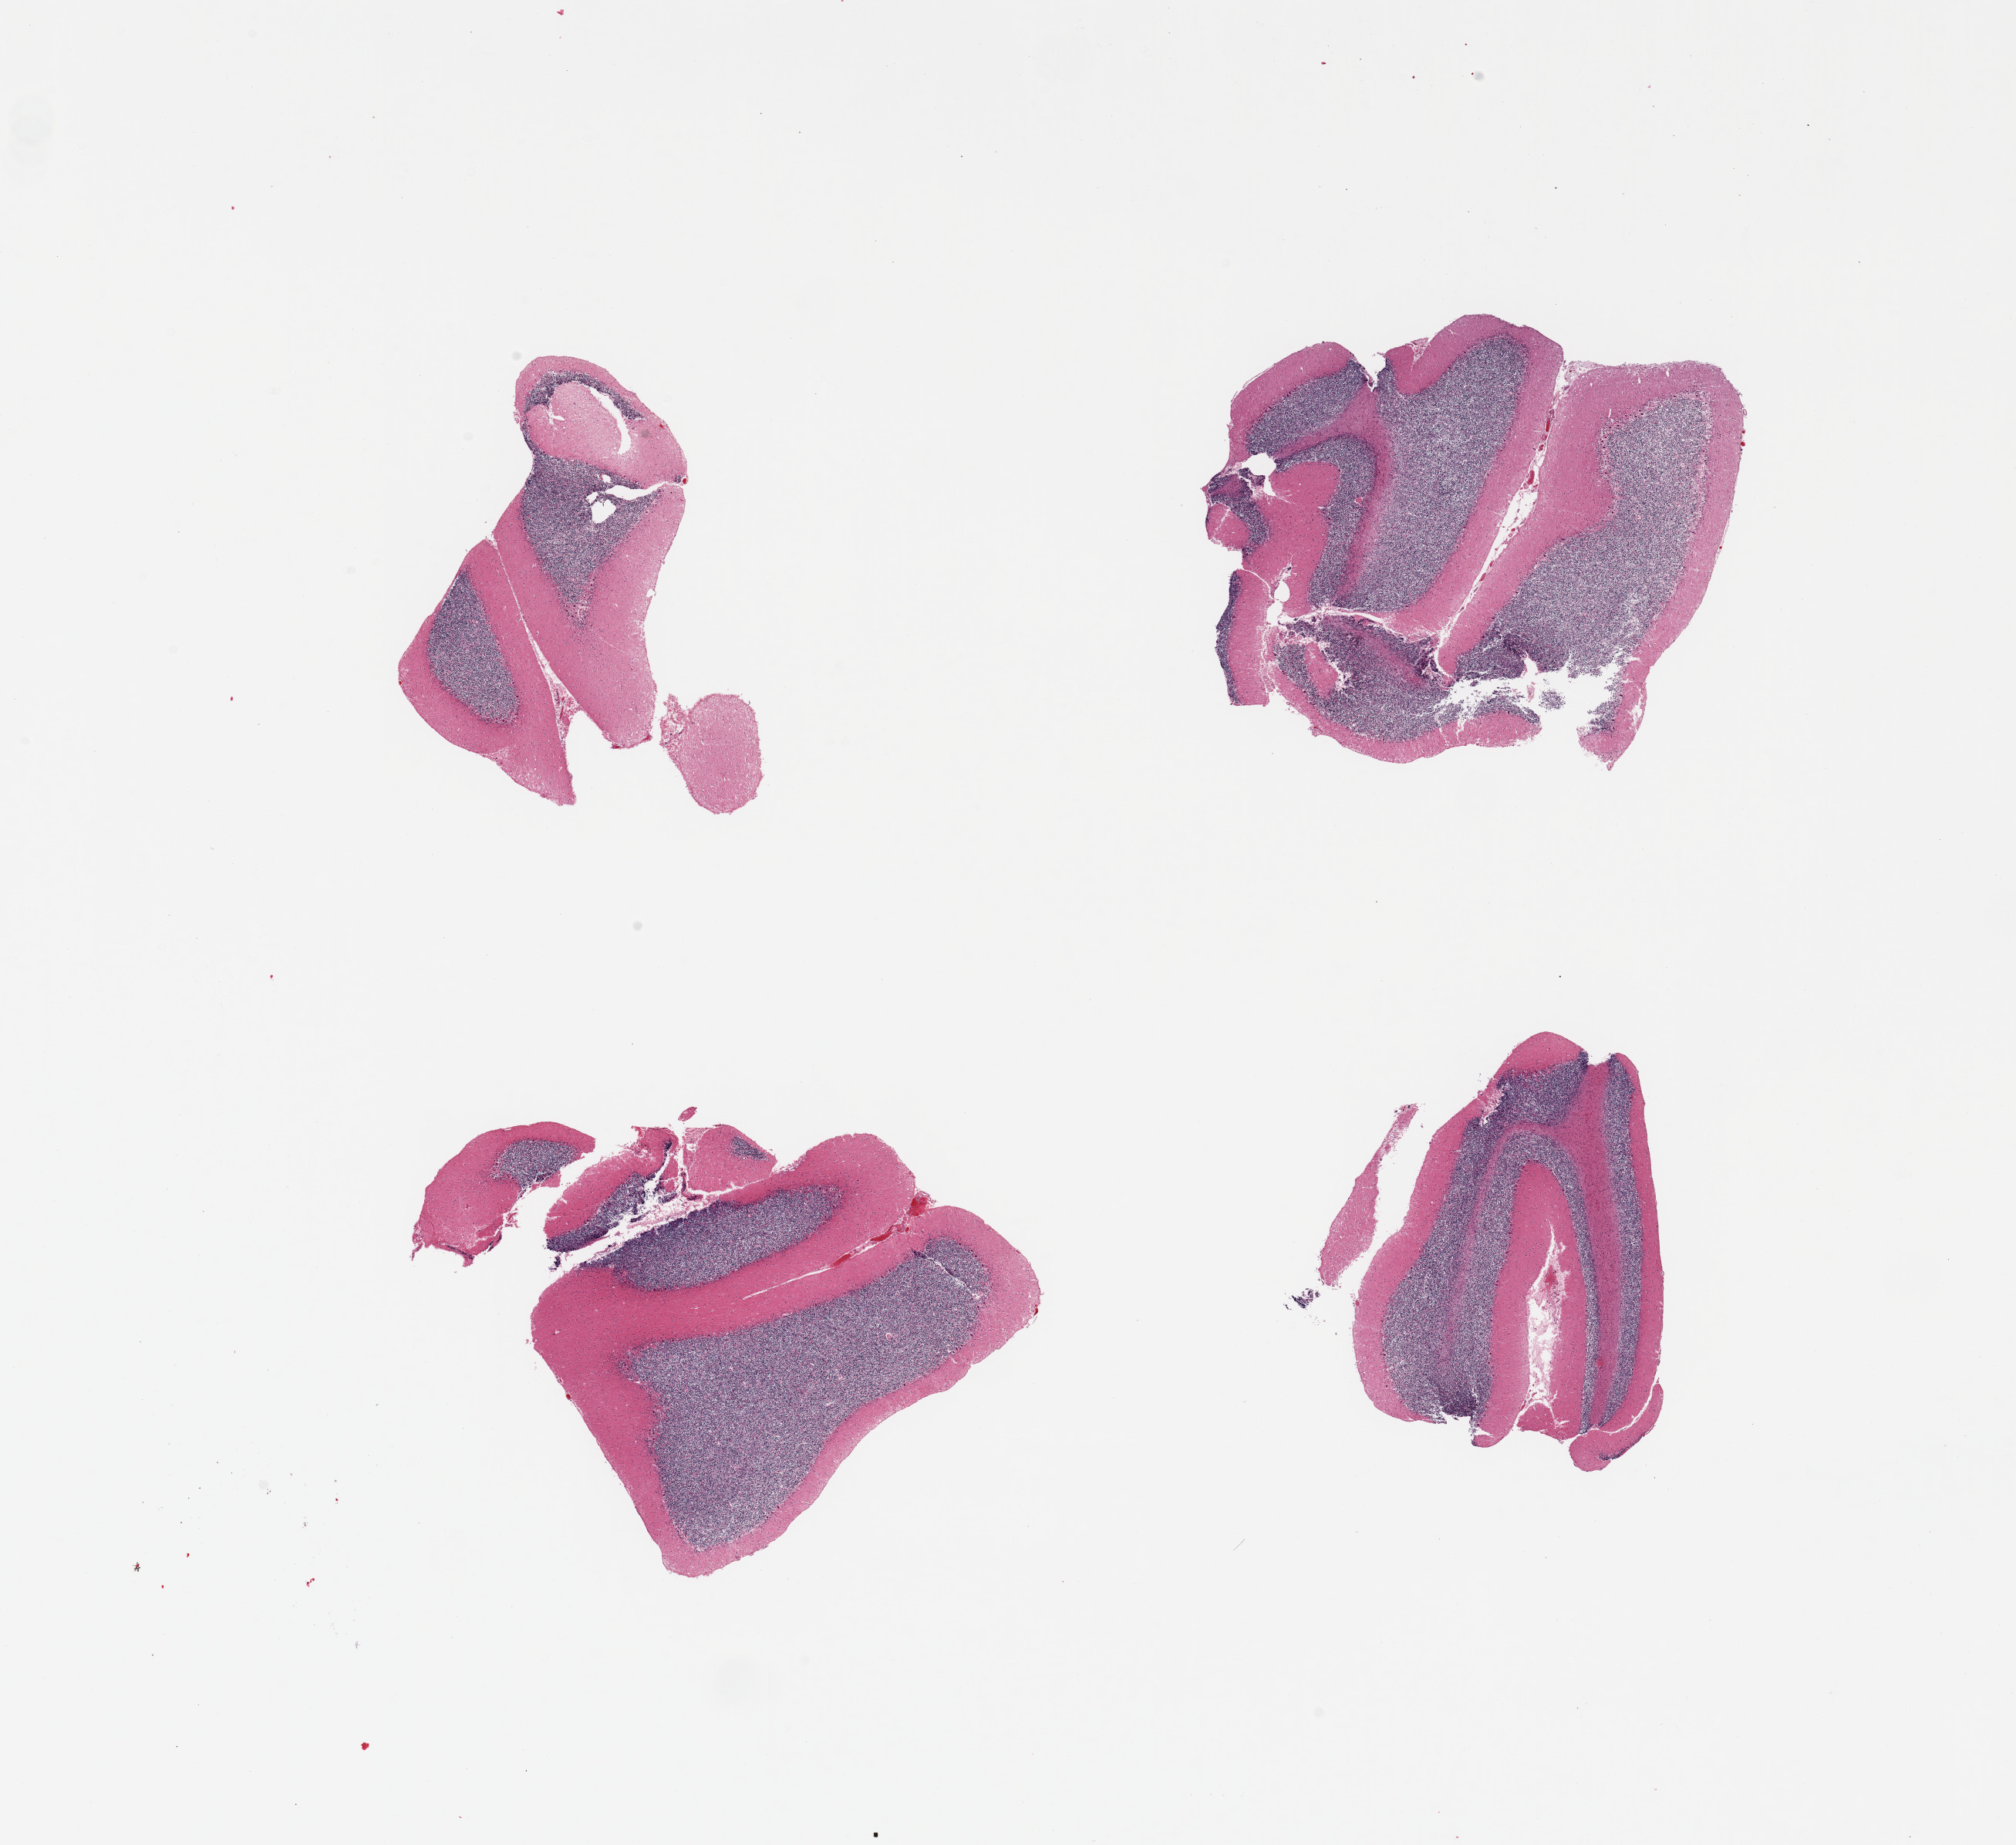
Whole-slide image, H&E stain — low-resolution overview of the scanned area, about 20.7 x 18.9 mm; PAXgene-fixed, paraffin-embedded tissue; section of cerebellum (target tissue); tissue donor sample. Donor sex: female.
- reviewer comment on this tissue sample: 4 pieces, no abnormalities